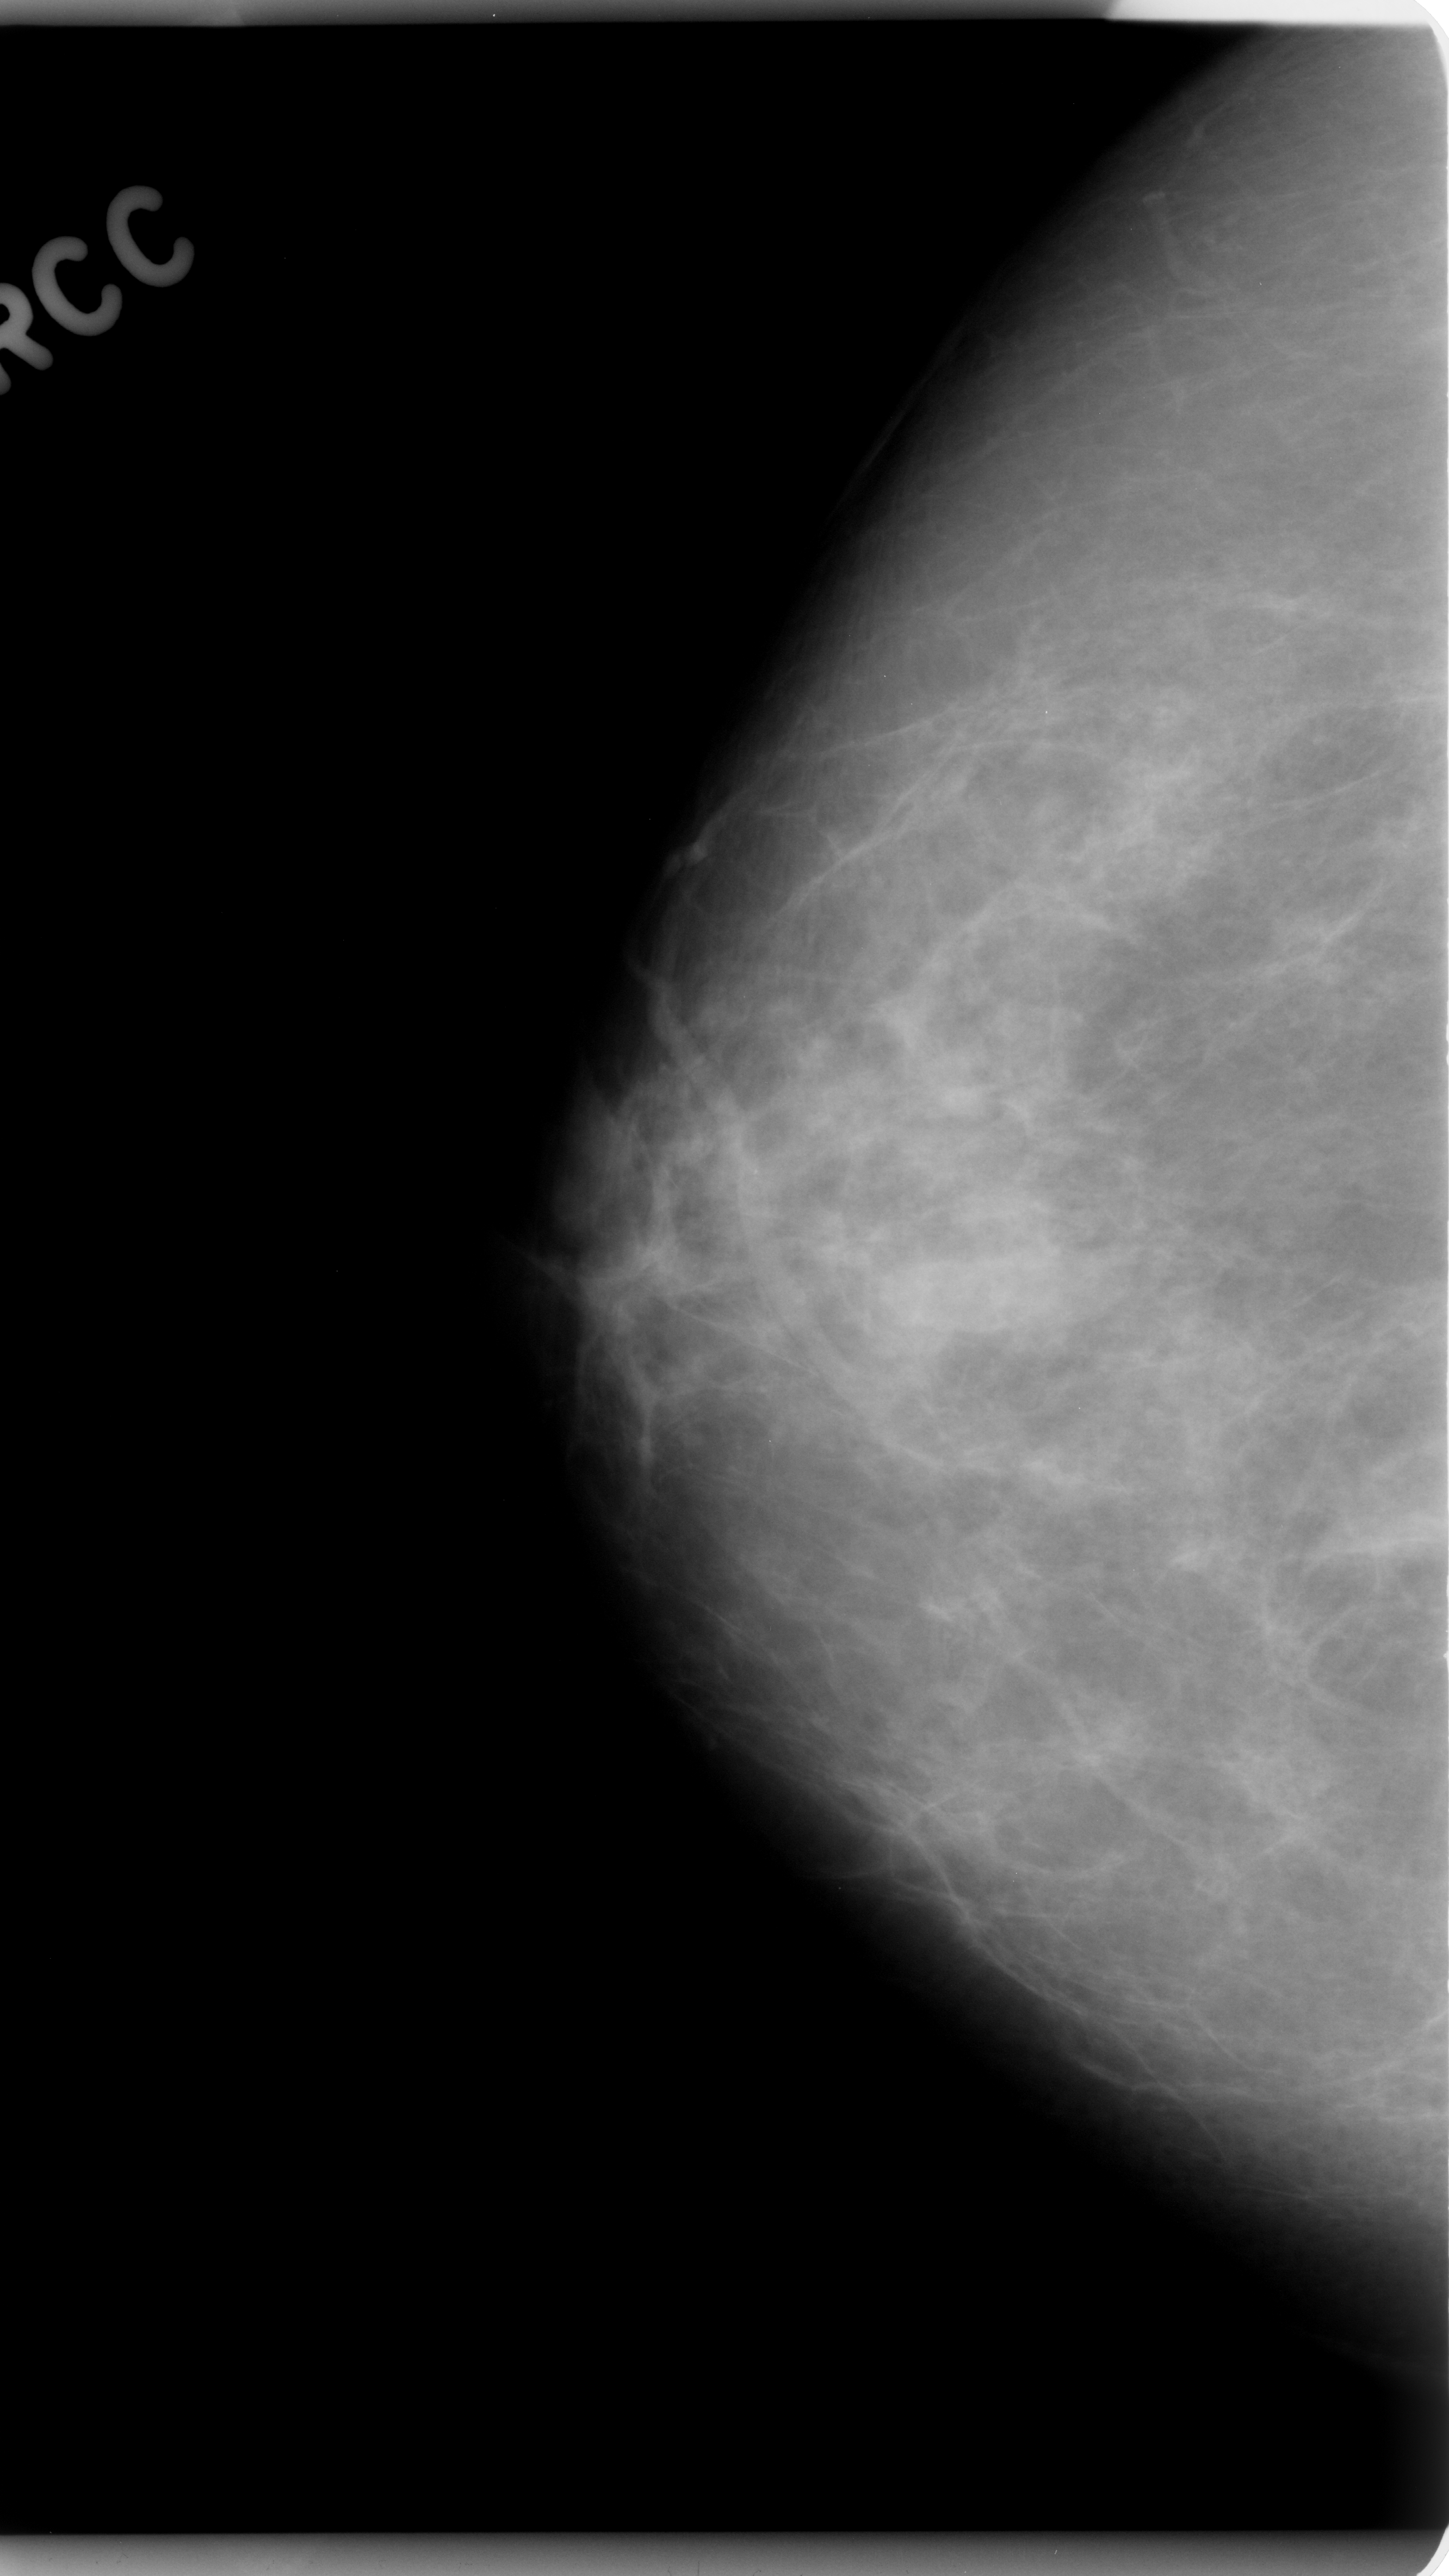
Mammogram (digitized film). Right breast. CC view. 1449 × 2576 image matrix.
Marked abnormalities (boxes around the expert regions of interest):
- mass, shape irregular, margins ill defined; BI-RADS assessment category 4; subtlety rating 3 on a 1 (subtle) to 5 (obvious) scale; pathology (as recorded): benign: bounding box (x1, y1, x2, y2) in pixels: (1352, 1375, 1449, 1670)